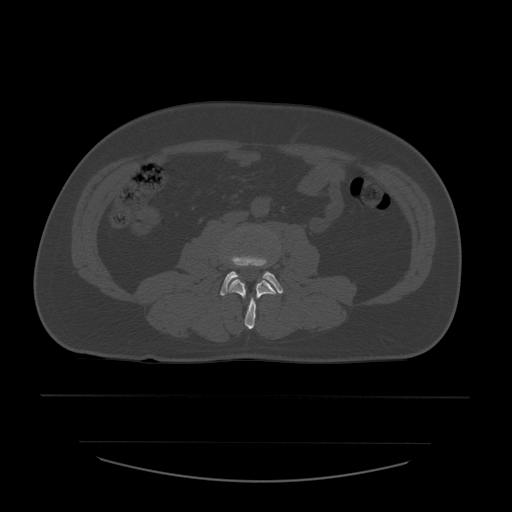
CT including the spine, one axial slice. 120 kVp. Bone window (W 1800 / L 400 HU). 1.25 mm slice thickness. 512 × 512 image matrix, field of view 441 × 441 mm. Patient age 44 years. From the clinical record (not read from this slice): primary cancer: soft tissue sarcoma.
Outlined on this slice (semi-automatically segmented with operator editing):
- L3 vertebra: bounding box <228,279,276,330> (left, top, right, bottom; pixels)
- L4 vertebra: <220,256,283,296>